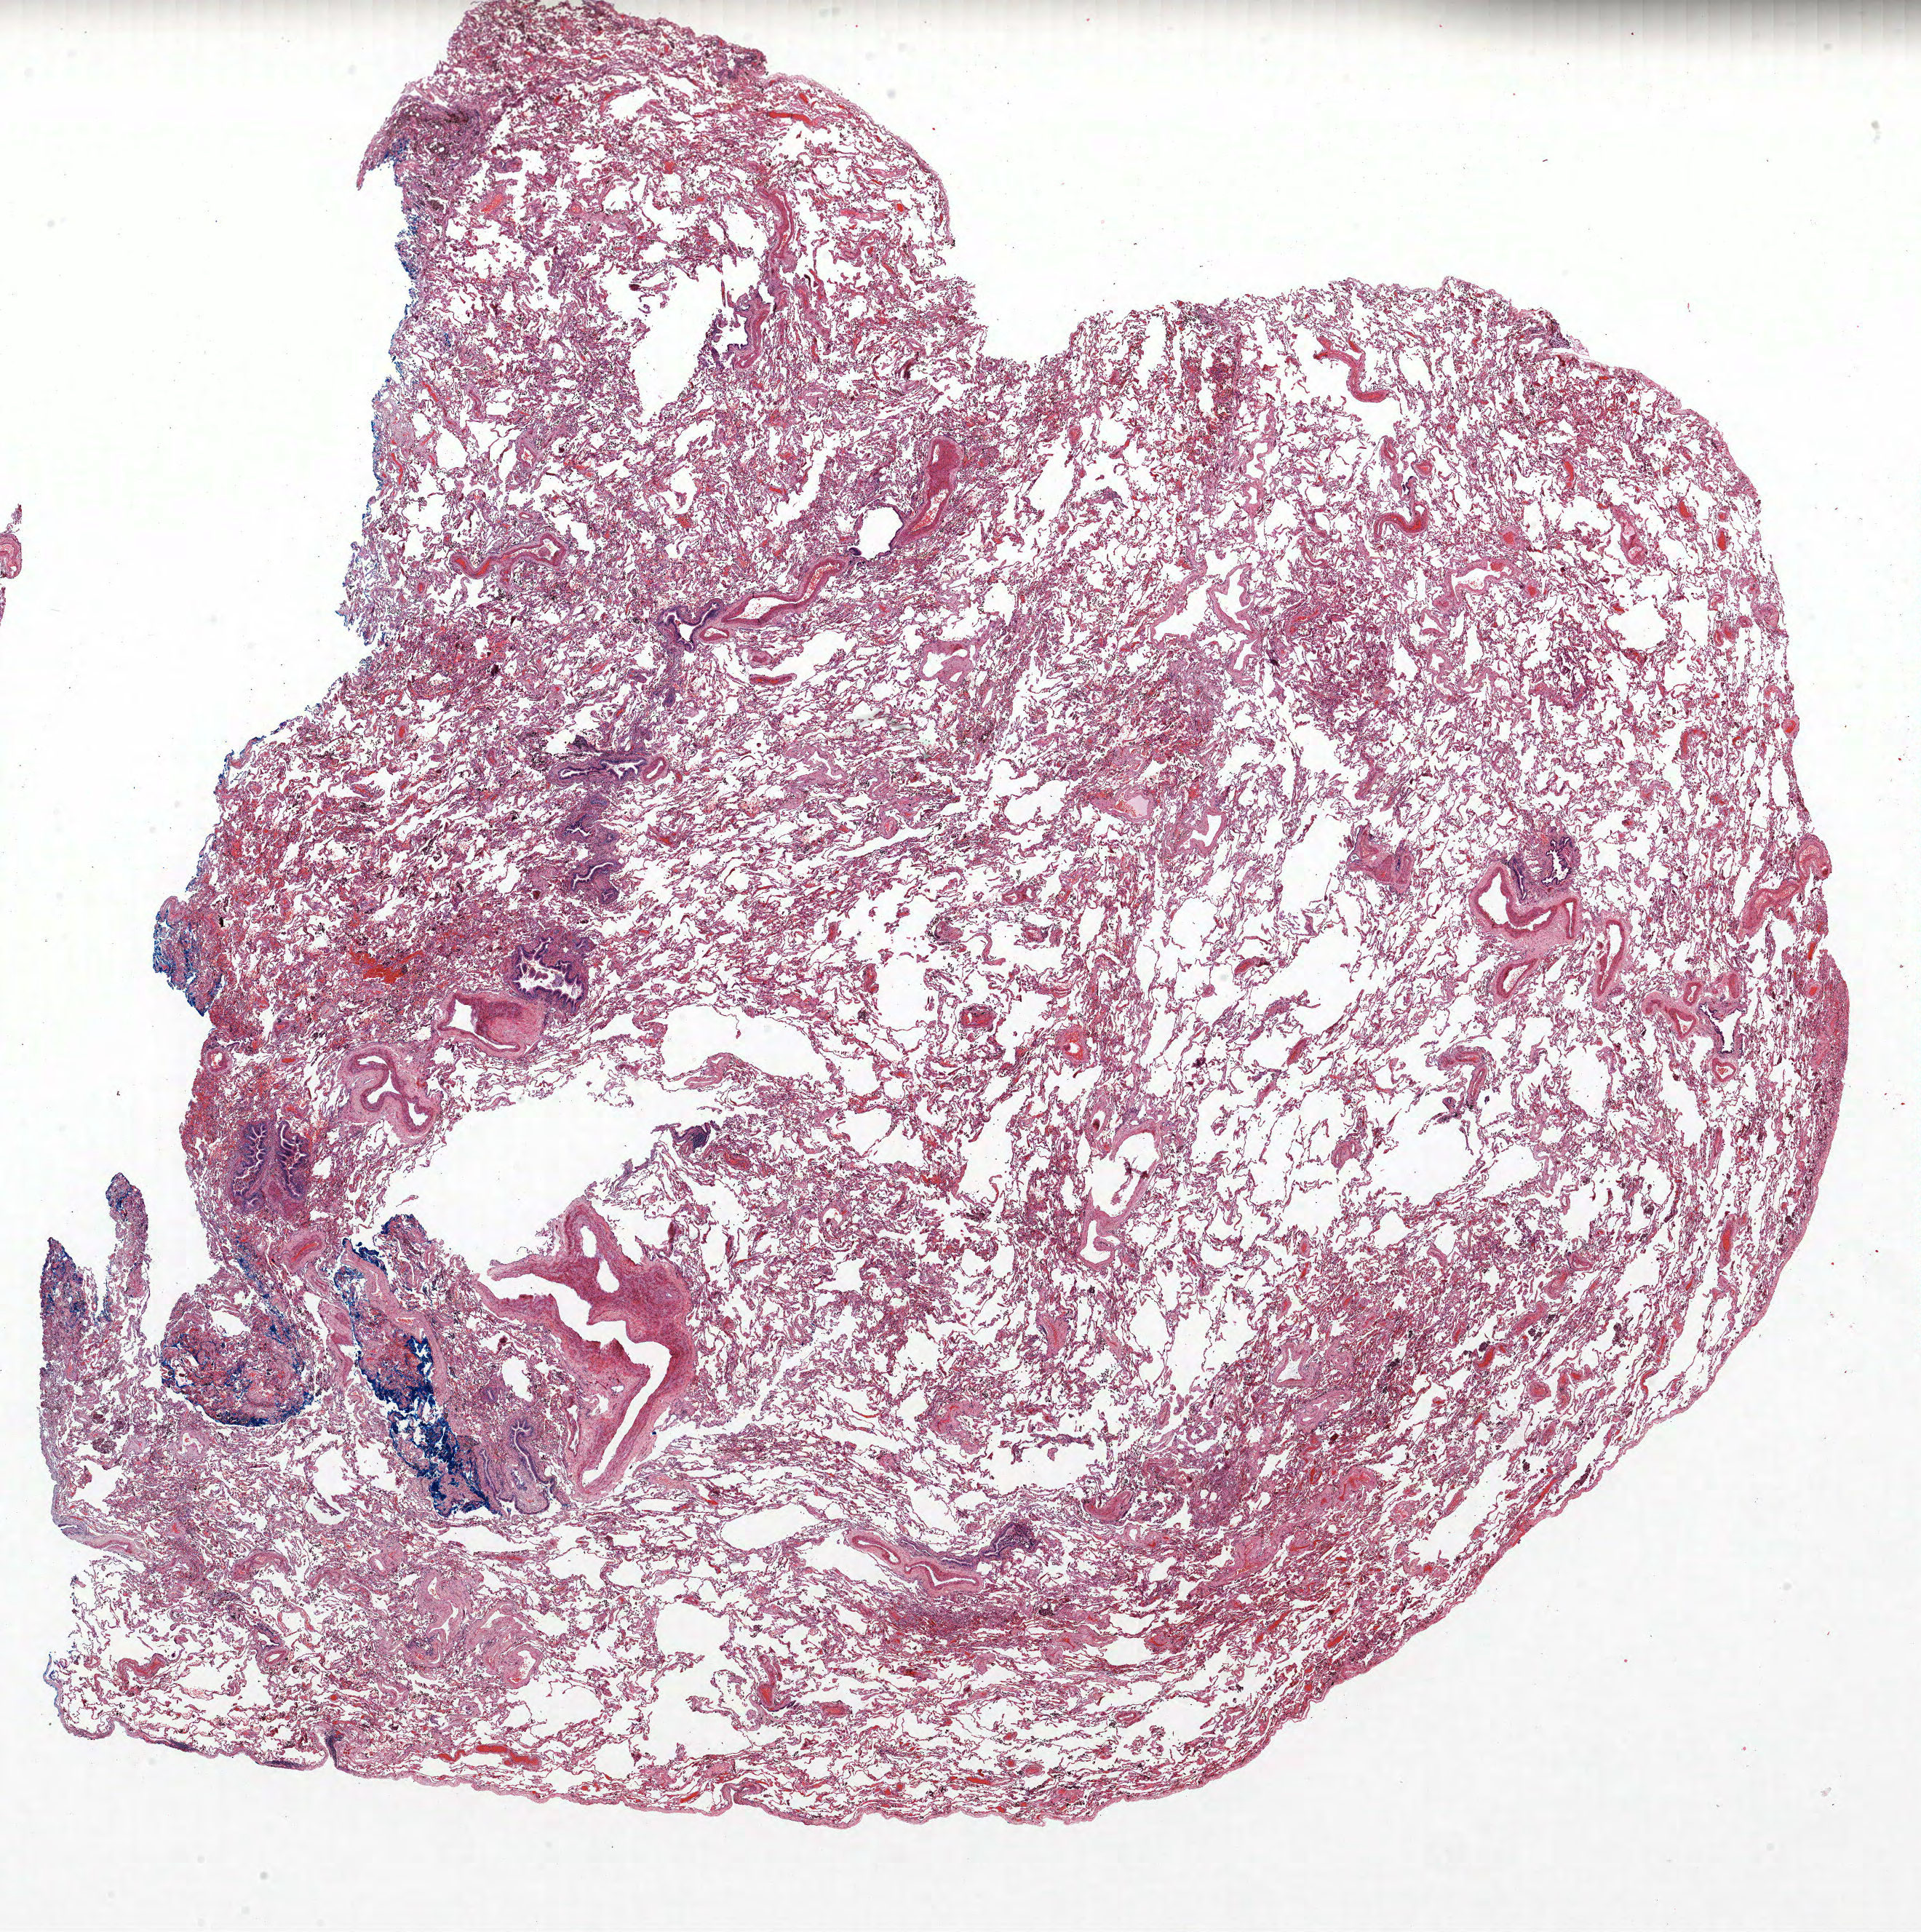
Whole-slide histology image, H&E, shown as a low-resolution overview of the whole scanned area (about 21.1 x 21.2 mm, acquisition: 40x scan), formalin-fixed paraffin-embedded (FFPE) section, lung. Female, age 58 at enrolment. Current smoker at enrolment.
Participant's lung-cancer diagnosis: Adenocarcinoma, NOS.